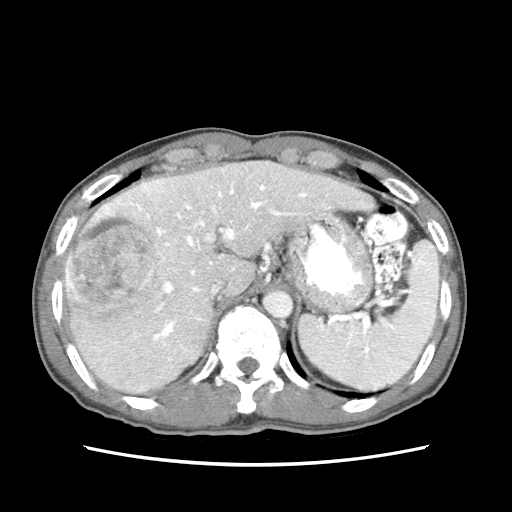
Contrast-enhanced abdominal CT (liver protocol), one axial slice; slice 52 of 79 in the series (ordered by position); 120 kVp; soft-tissue window (W 400 / L 40 HU); 2.5 mm slice thickness; 512 × 512 image matrix, field of view 320 × 320 mm. From the clinical record (not read from this slice): diagnosis: hepatocellular carcinoma (patient treated with transarterial chemoembolisation; whether this scan precedes or follows treatment is not stated here); TNM stage (as recorded): Stage-IIIB.
Outlined on this slice (semi-automatically segmented with operator editing):
- liver parenchyma outside the tumour (the mass and vessels are separate outlines, so this box may not span the whole liver): bounding box (x1, y1, x2, y2) in pixels: (64, 160, 374, 394)
- mass: (65, 193, 166, 312)
- liver vessels: (104, 180, 318, 360)